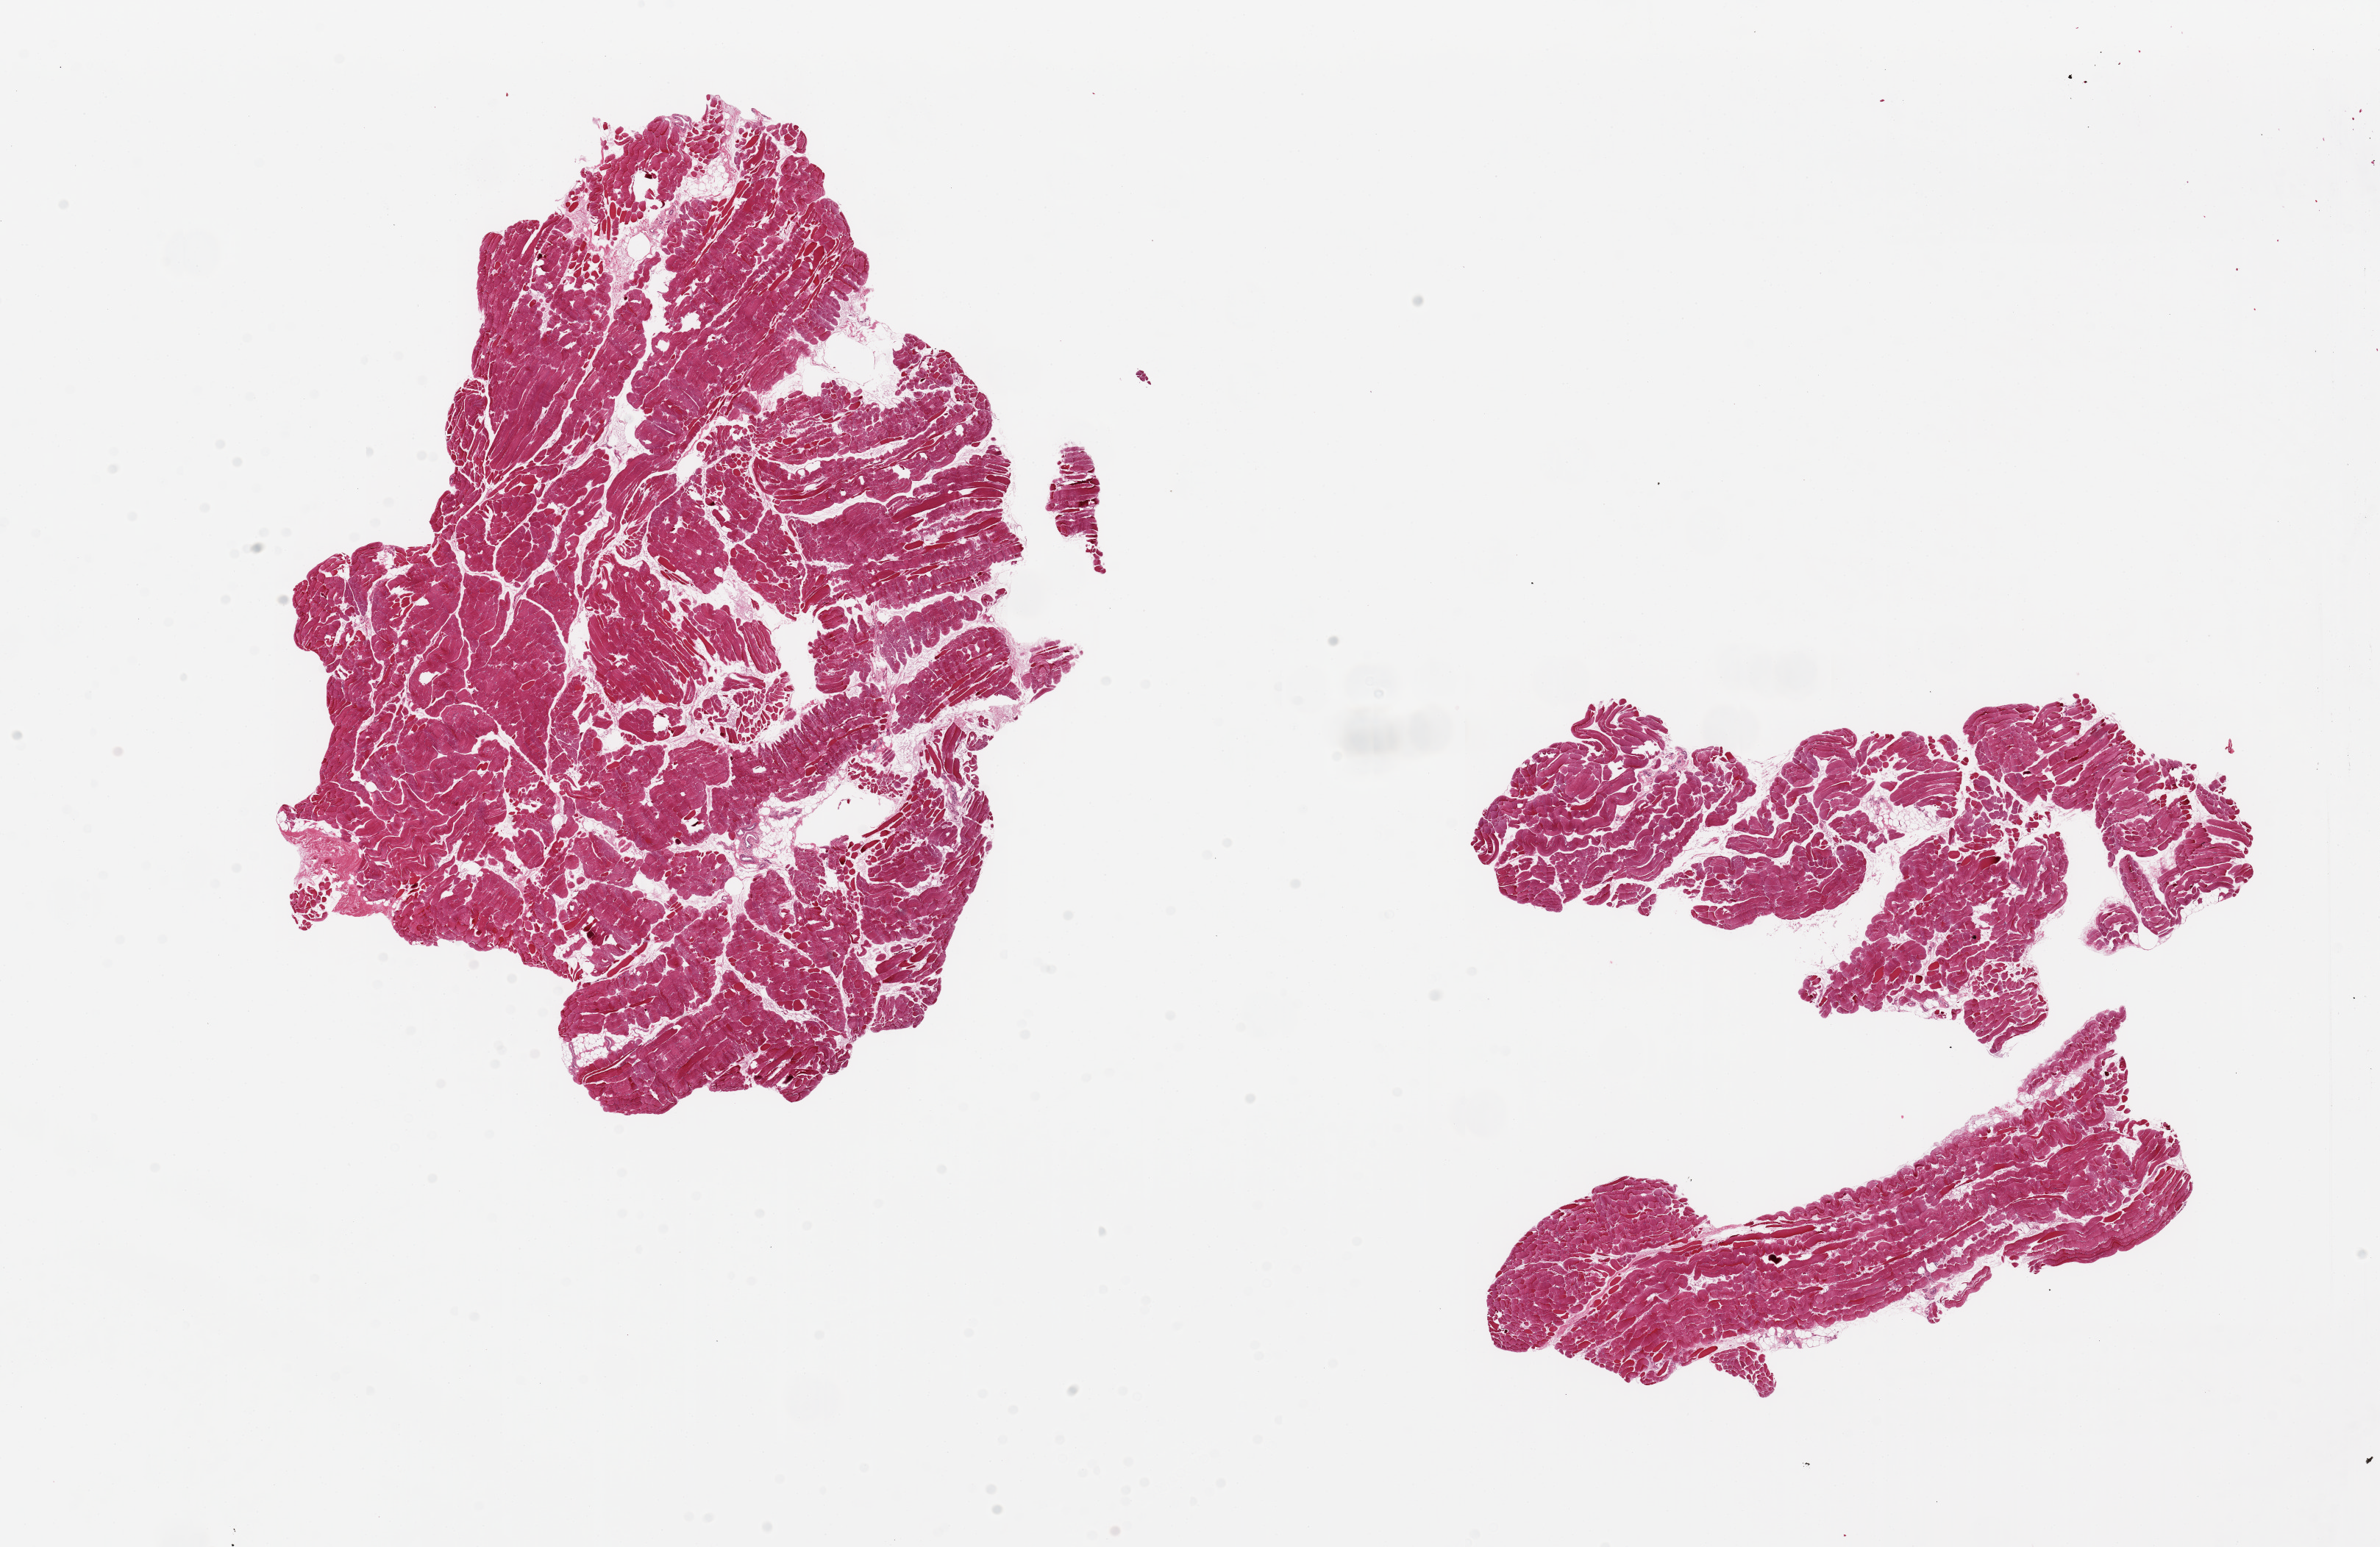
Whole-slide image, H&E stain, brightfield — whole scanned area (about 25.6 x 16.6 mm) shown as a low-resolution overview. PAXgene-fixed paraffin-embedded (PFPE) section. Section of skeletal muscle (target tissue). Tissue donor sample.
Pathologist's review note for this sample: 2 pieces. 11x9 & 9x8mm; well trimmed.